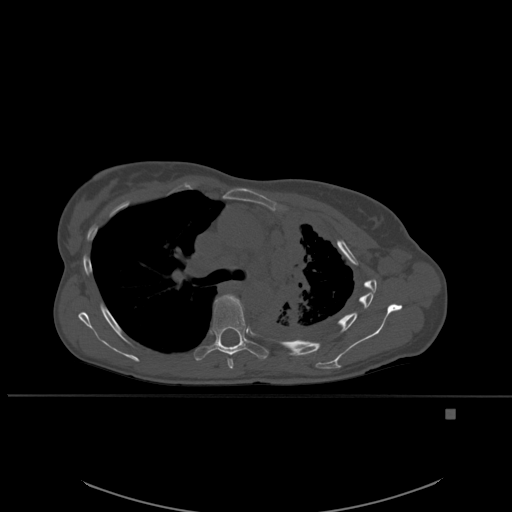
CT including the spine, one axial slice; slice 386 of 537 in the series (ordered by position); bone window (W 1800 / L 400 HU); 1.5 mm slice thickness; 512 × 512 image matrix, field of view 440 × 440 mm. Patient: female, 45 years. From the clinical record (not read from this slice): primary cancer: lung.
Annotated regions visible in this slice (semi-automatically segmented with operator editing):
- T5 vertebra: box from (x=216, y=294) to (x=240, y=369) px
- T6 vertebra: (x=196, y=298)–(x=269, y=362)